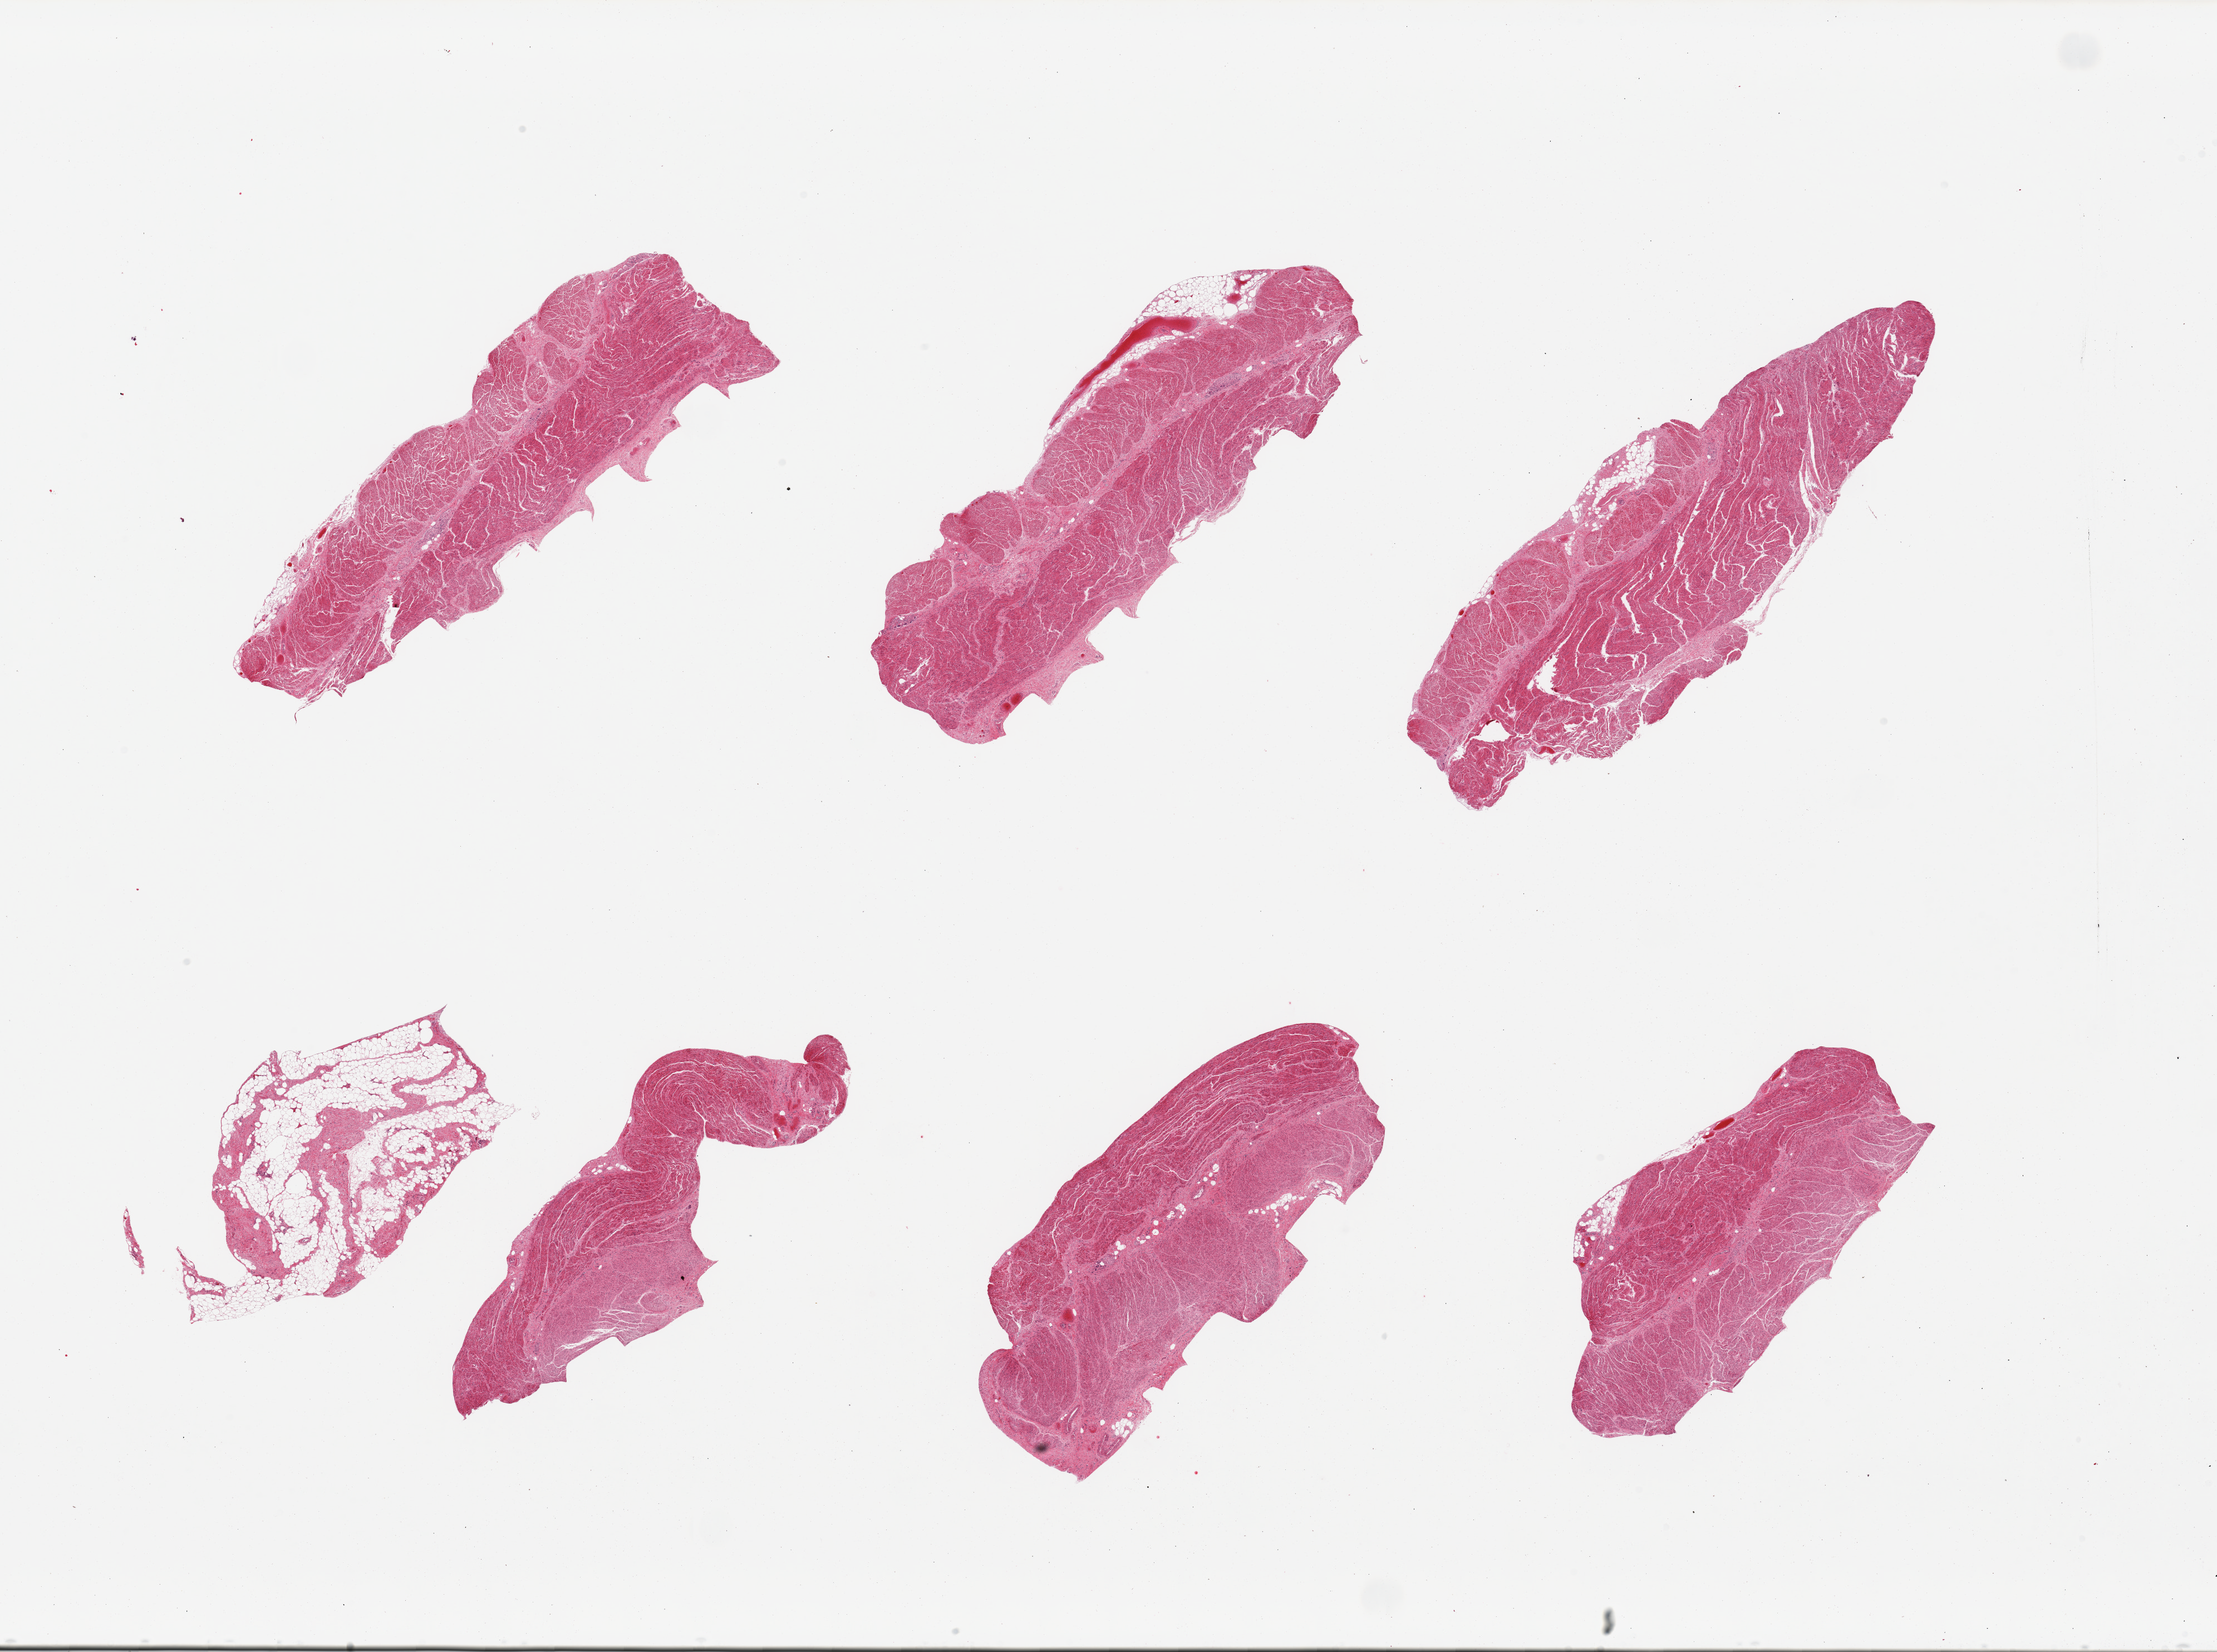
Digitized haematoxylin and eosin-stained section, brightfield, a low-resolution overview of the entire scanned area, about 31.5 x 23.5 mm, PAXgene-fixed, paraffin-embedded tissue, sampled site (target tissue): gastroesophageal junction, donor tissue sample. Donor sex: male.
Reviewer comment on this tissue sample: 7 pieces; 1 piece is fibrofatty tissue.